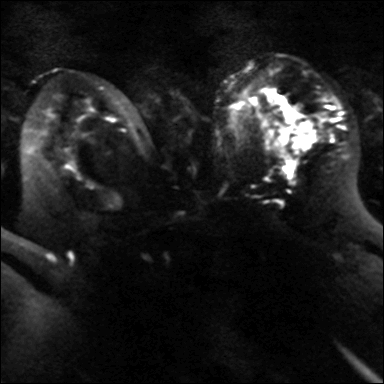
Breast MRI, one axial slice. Slice 25 of 40 in the series (ordered by position). Diffusion-weighted series; image 2 of 4 stored at this slice position (different b-values; order by instance number). 3 T. 384 × 384 image matrix, field of view 320 × 320 mm. Female patient.
Outlined on this slice (outlined manually by an expert reader):
- tumour on diffusion-weighted imaging: bounding box (x1, y1, x2, y2) in pixels: (291, 121, 315, 153)